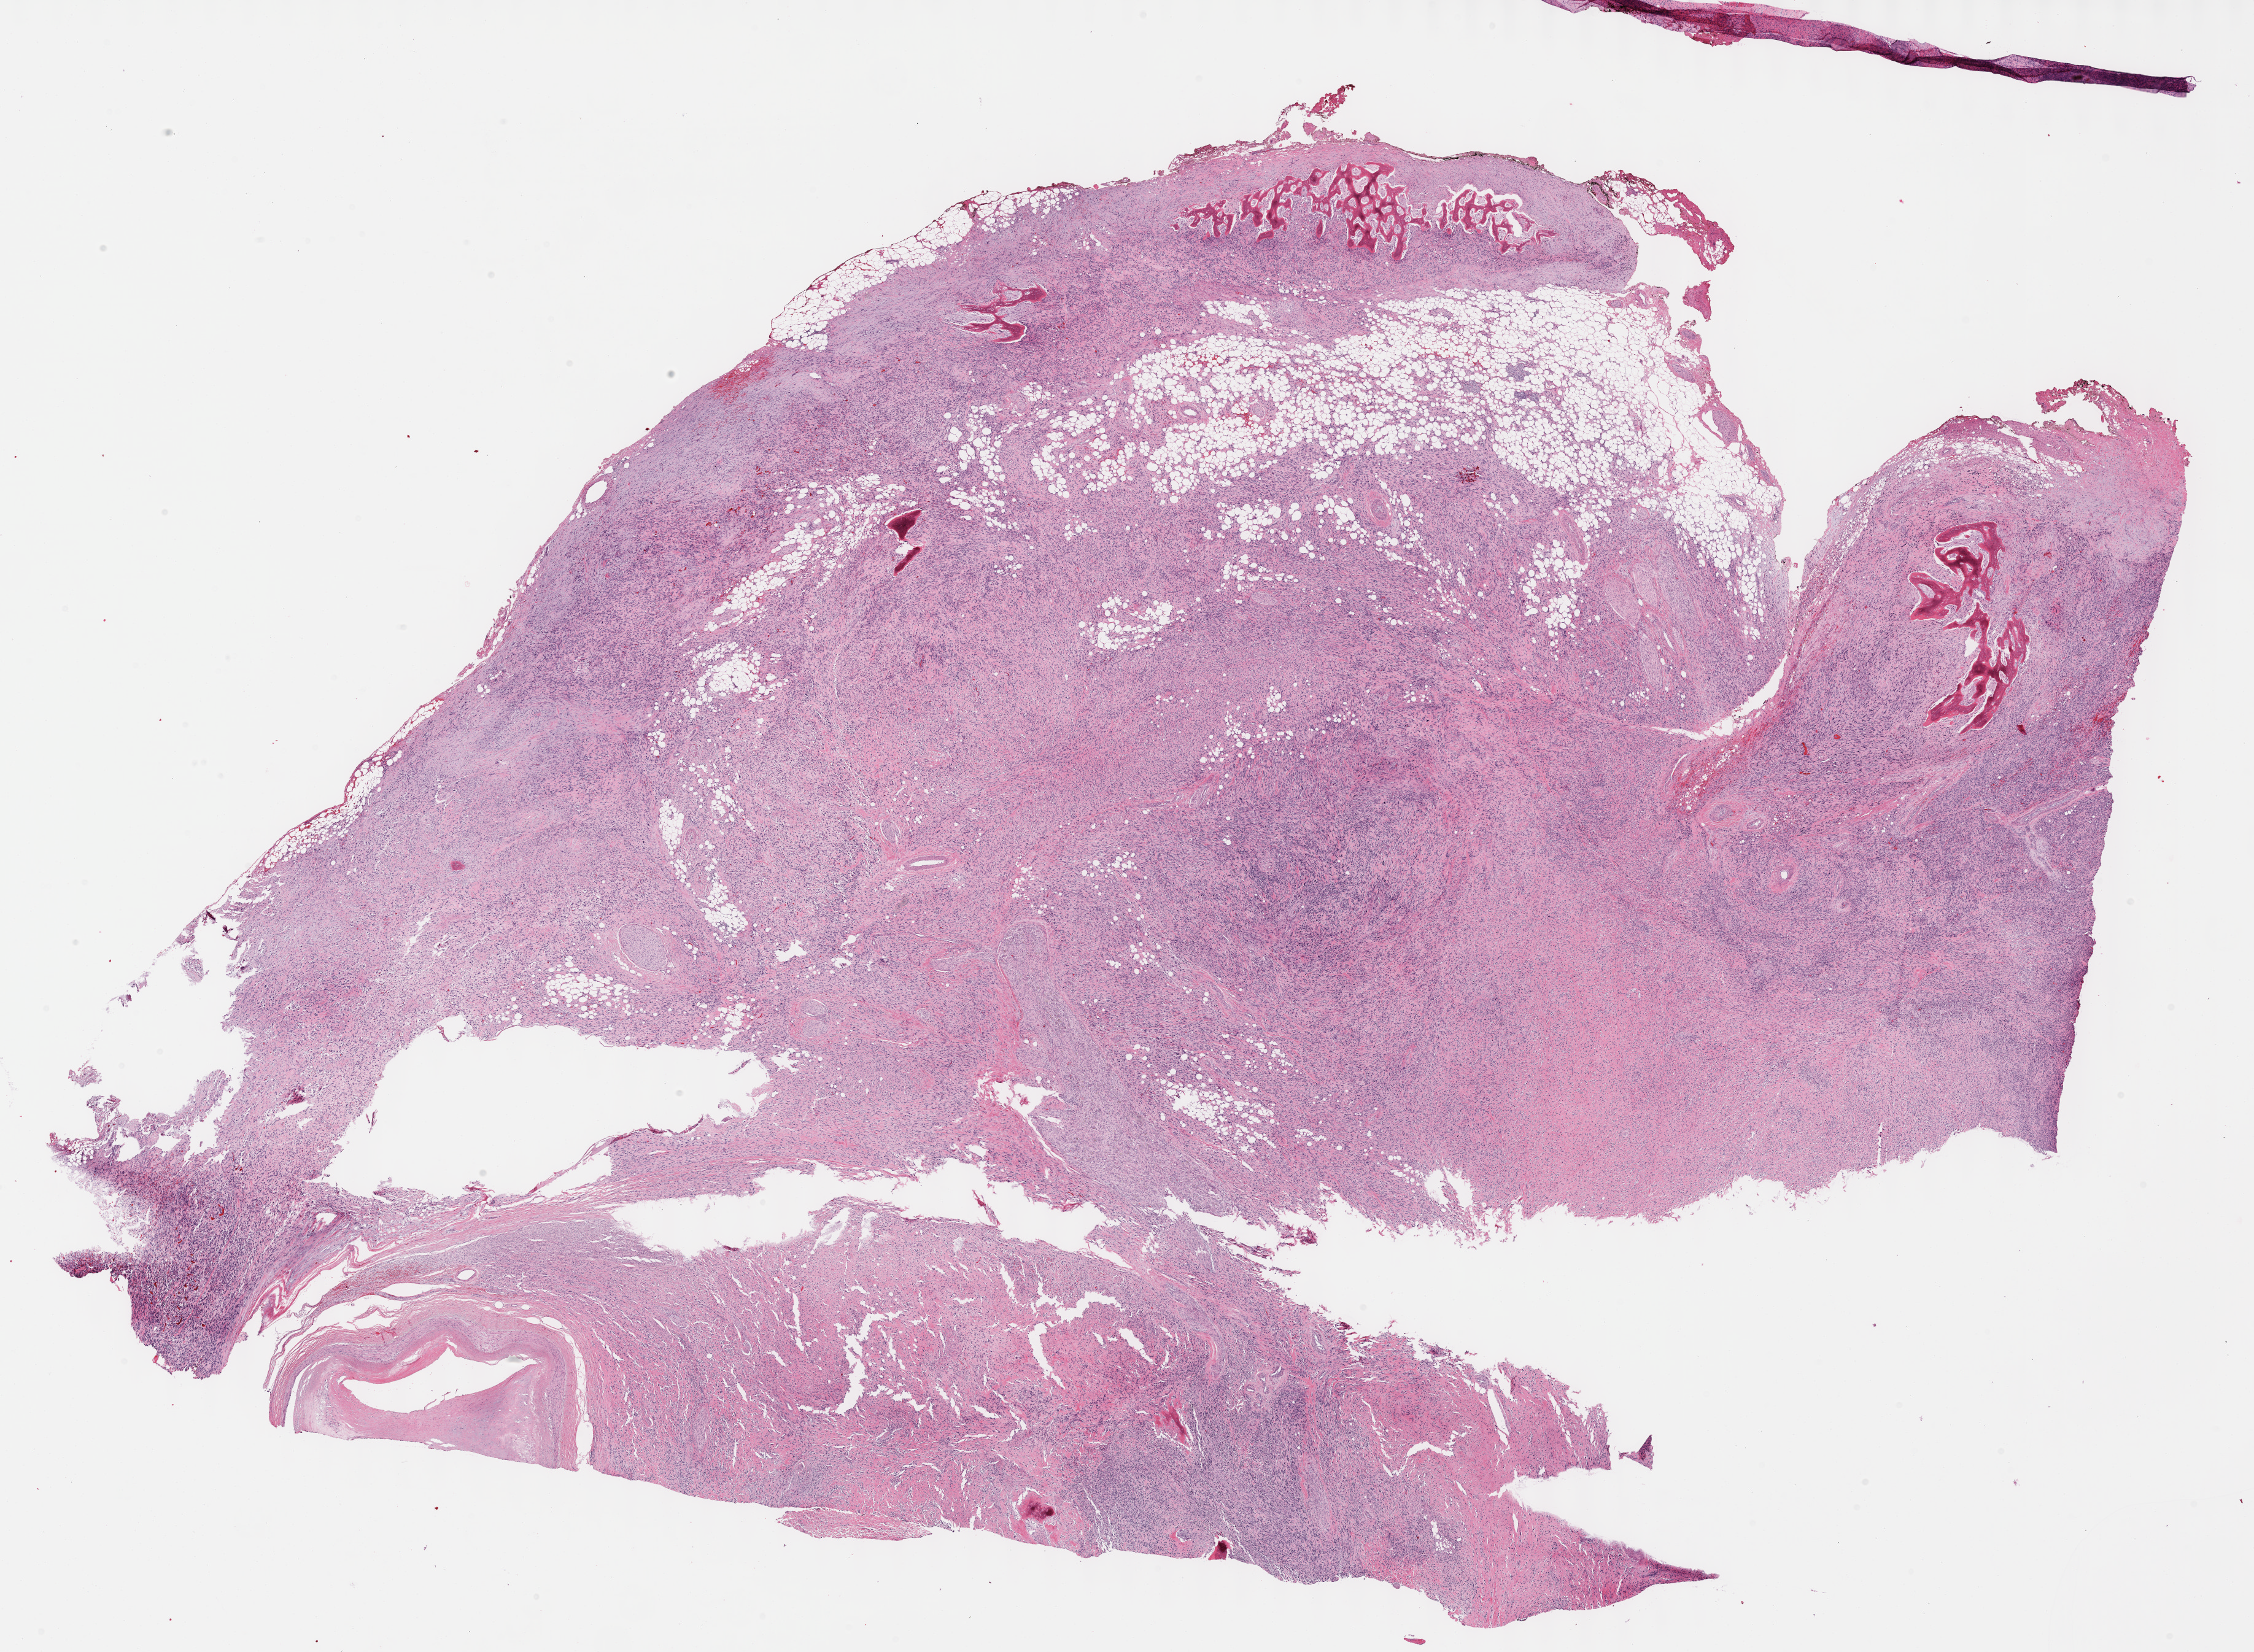
Hematoxylin and eosin (H&E) stained whole-slide image — low-resolution overview of the scanned area, about 29.7 x 21.8 mm (from a 40x scan); formalin-fixed paraffin-embedded (FFPE) diagnostic section; retroperitoneum and peritoneum, primary tumour sample. Male patient; age at initial diagnosis 72 years.
Pathologic diagnosis: Sarcoma, NOS.